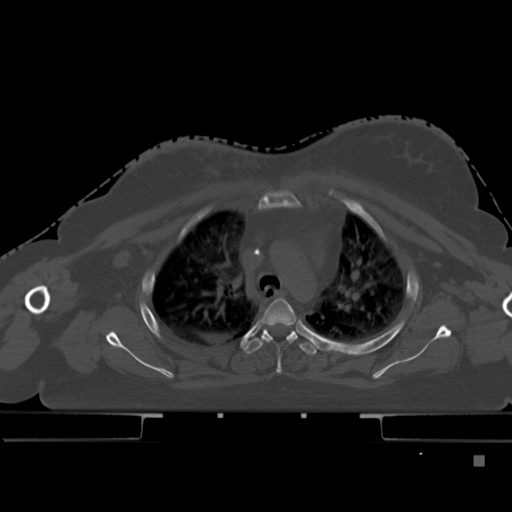
CT including the spine, one axial slice. Slice 339 of 495 in the series (ordered by position). Bone window (W 1800 / L 400 HU). 1.5 mm slice thickness. 512 × 512 image matrix. Patient: female, 33 years. Case-level facts recorded for this patient, not image findings: primary cancer: breast; vertebrae with lytic lesions (as recorded): T1.
Outlined on this slice (semi-automatically segmented with operator editing):
- T3 vertebra: bounding box <261,297,296,373> (left, top, right, bottom; pixels)
- T4 vertebra: <244,328,319,355>